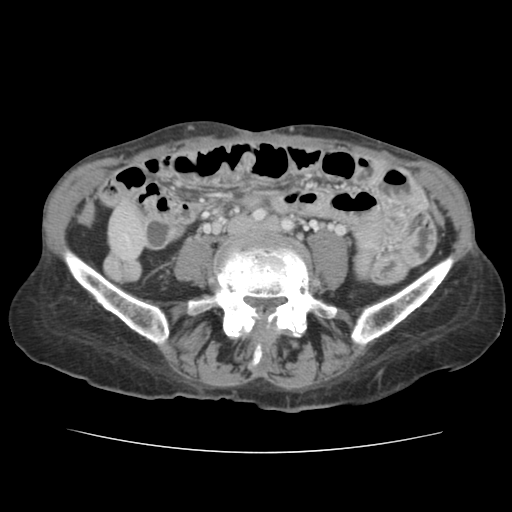
Contrast-enhanced abdominal CT, one axial slice. Position 11 of 136 along the scan axis. 120 kVp. Intravenous contrast given. Soft-tissue window (W 400 / L 40 HU). 2.5 mm slice thickness. 512 × 512 image matrix, field of view 319 × 319 mm. Female patient, age 77 years. From the clinical record (not read from this slice): diagnosis: colorectal cancer liver metastases, imaged before liver resection; multiple liver metastases: yes; largest metastasis: 3 cm; disease in both lobes: no.
Structures marked on this image (manually delineated by an expert):
- liver: box from (x=111, y=209) to (x=145, y=258) px